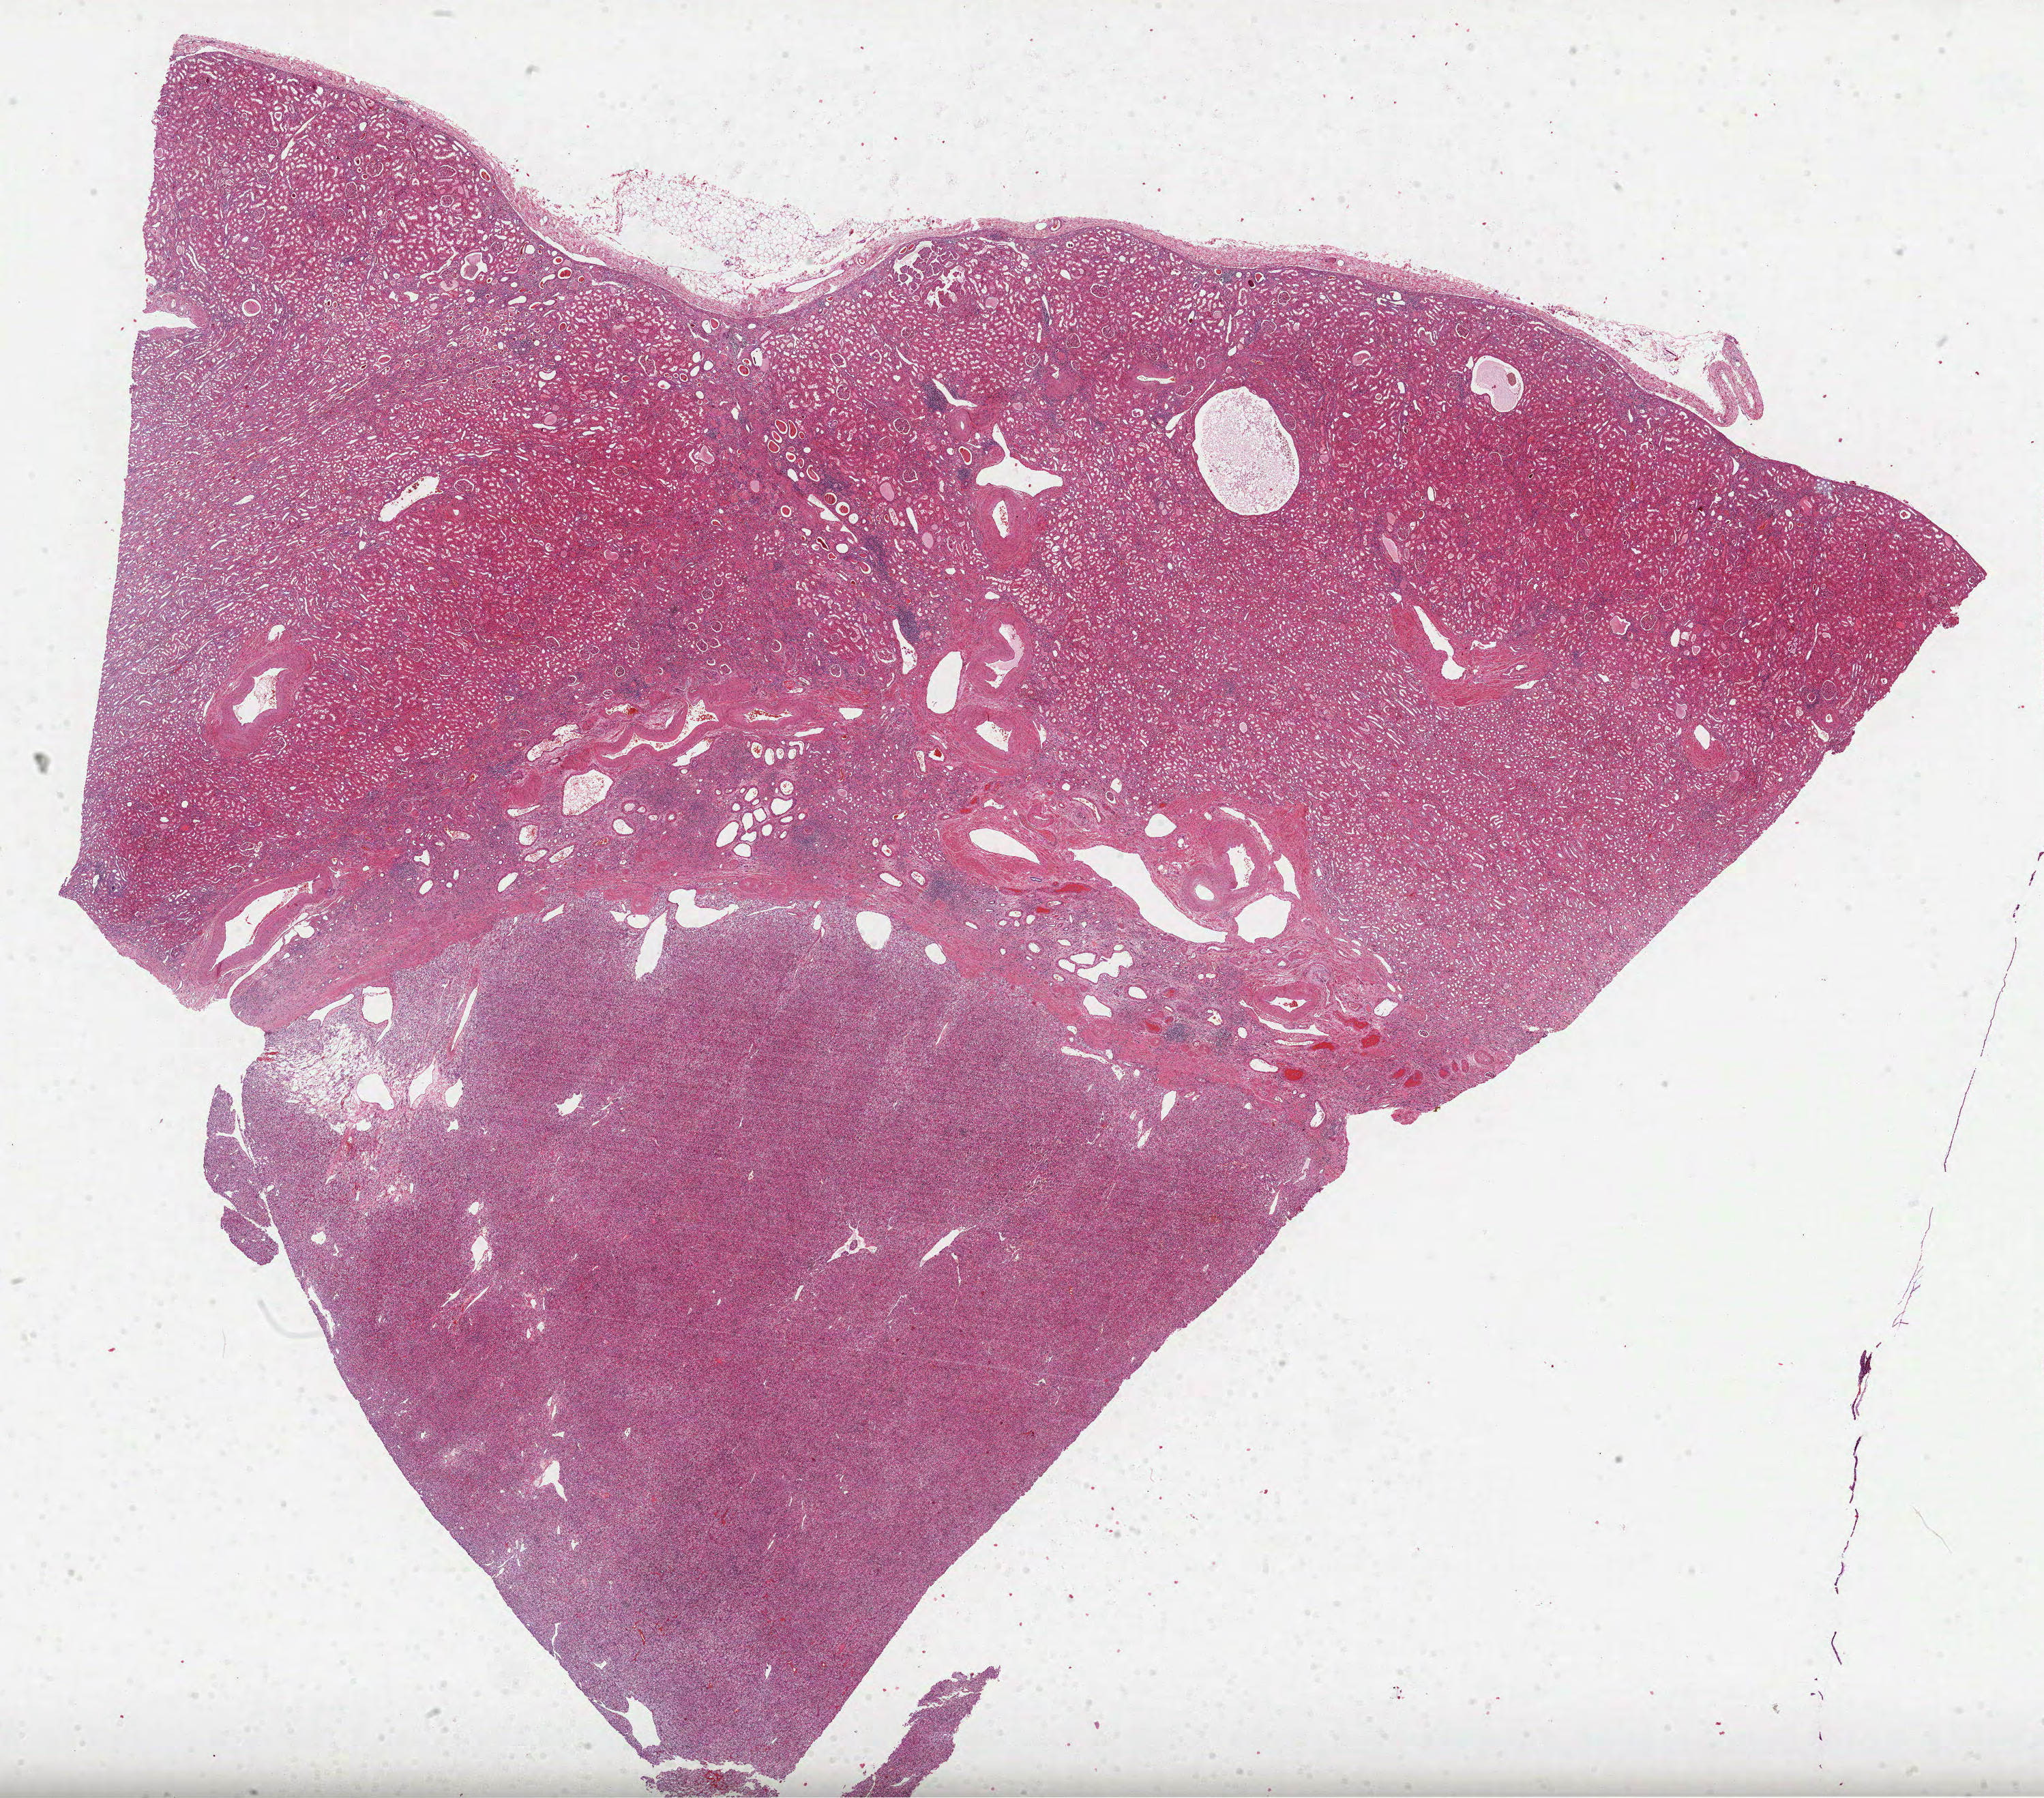
Whole-slide histology image, Hematoxylin and eosin (H&E) stained — whole scanned area (about 24.2 x 21.3 mm) shown as a low-resolution overview; formalin-fixed paraffin-embedded (FFPE) diagnostic section; primary tumour sample from the kidney. Female, age 65 years at initial diagnosis. Histologic grade: G2 (moderately differentiated).
* AJCC pathologic stage: I (5th edition)
* laterality: left
* diagnosis: Clear cell adenocarcinoma, NOS
* TNM: T1 N0 M0